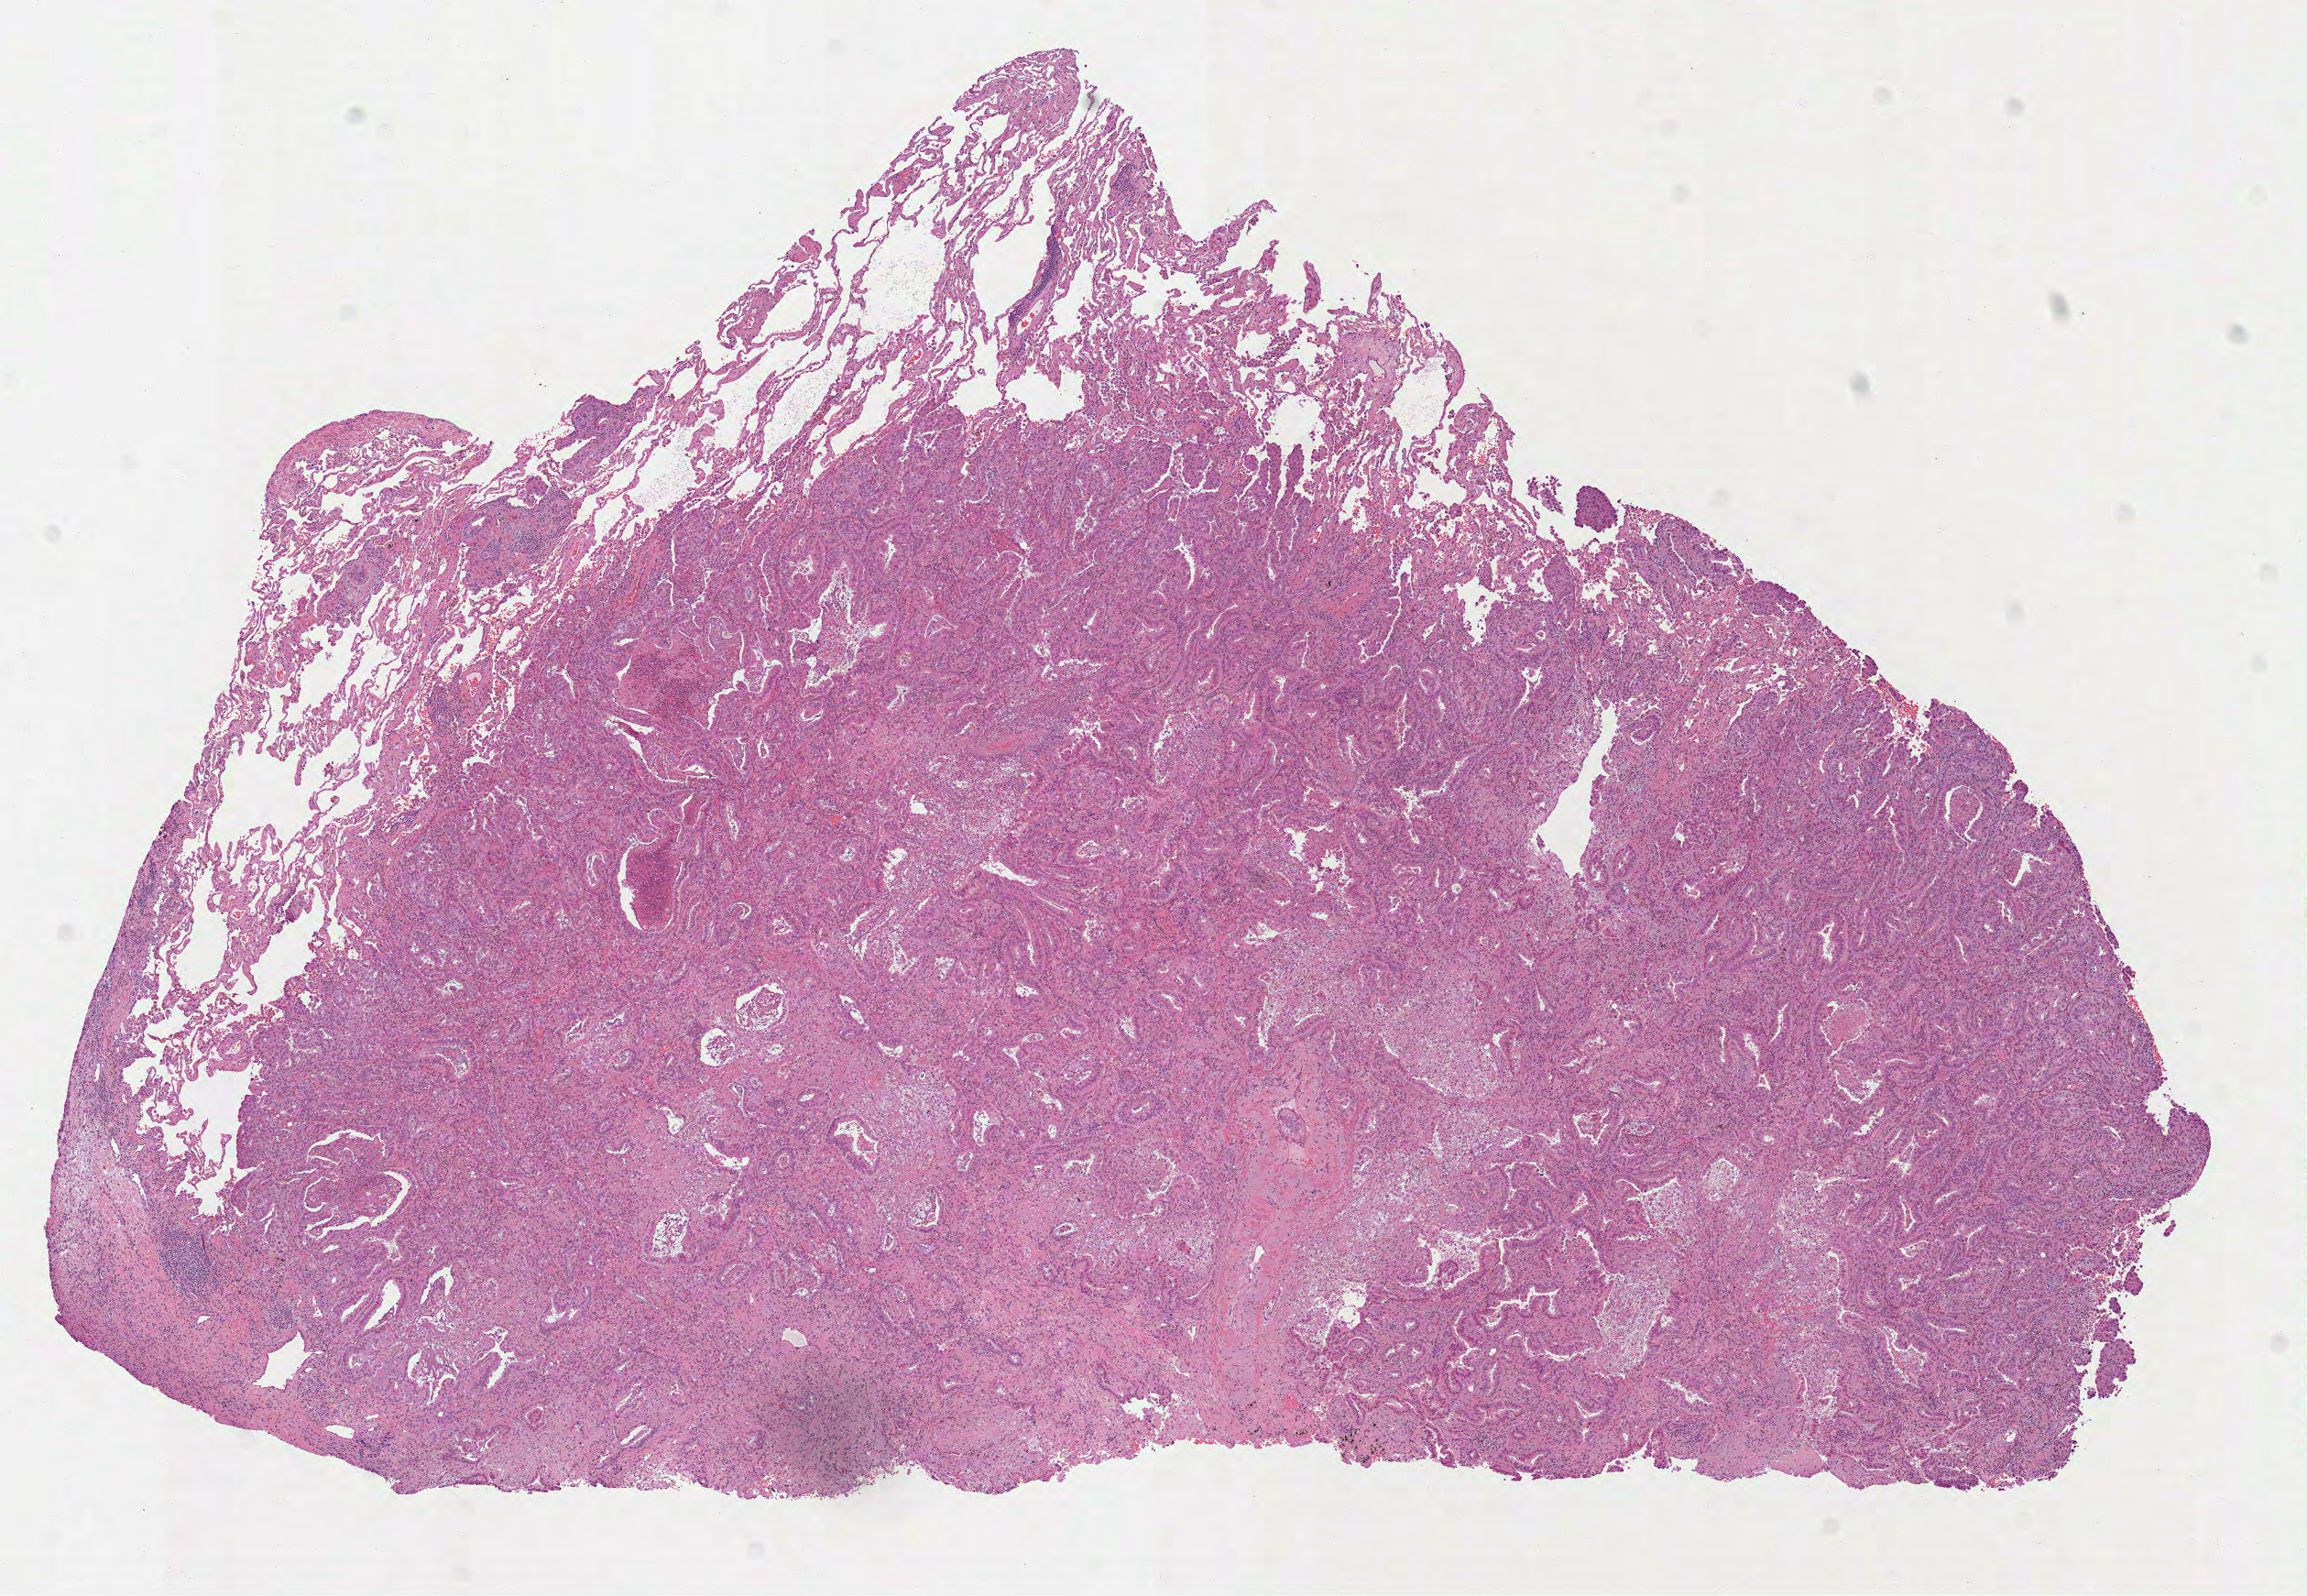
H&E whole-slide image — whole scanned area (about 10.2 x 7.0 mm) shown as a low-resolution overview; formalin-fixed paraffin-embedded (FFPE) diagnostic section; sample: primary tumour, lung. Female patient; age at initial diagnosis 67 years.
- AJCC pathologic stage: IB
- laterality: left
- histologic diagnosis: Adenocarcinoma, NOS (upper lobe, lung)